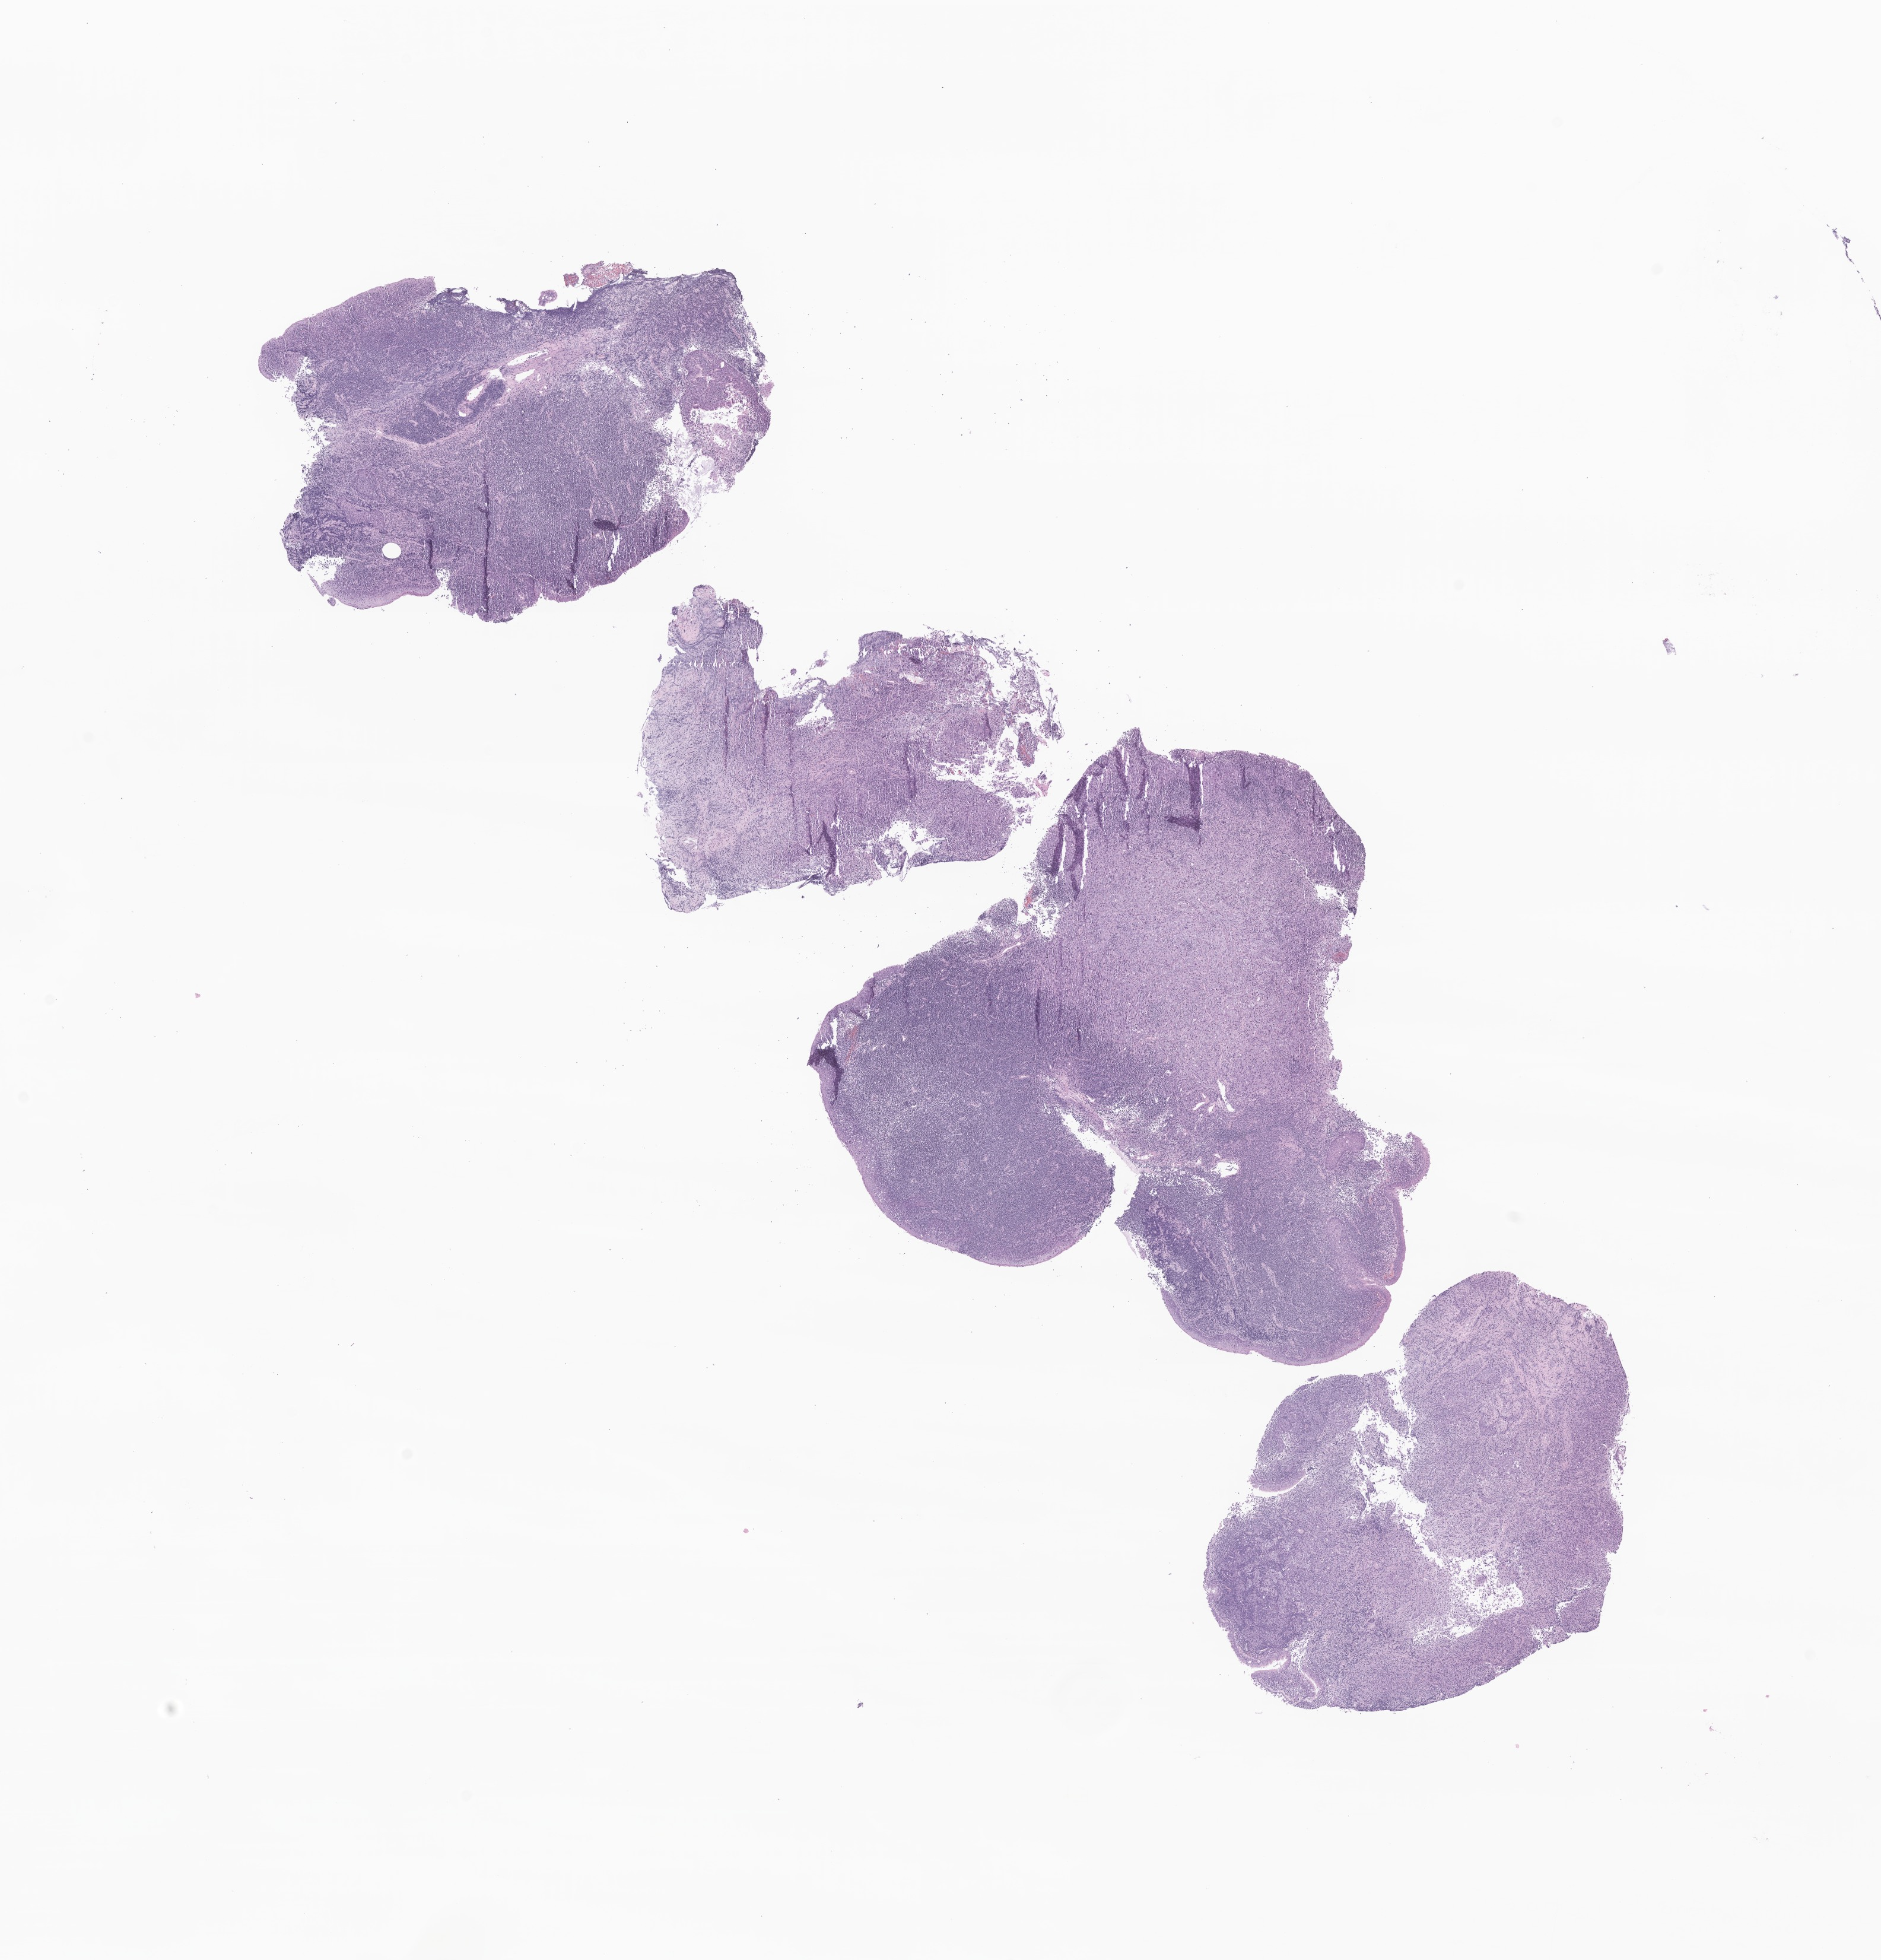
H&E whole-slide image of tumor tissue from the nasal cavity — a low-resolution overview of the entire scanned area, about 13.4 x 13.9 mm, formalin-fixed, paraffin-embedded (FFPE) tissue. Patient: male, age 205 months (17 years 1 month).
• recorded diagnosis: Carcinoma, NOS